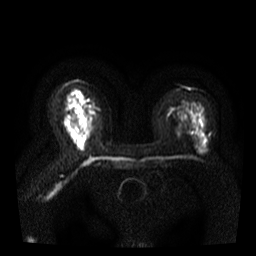
Breast MRI, one axial slice. Slice 20 of 40 in the series (ordered by position). Diffusion-weighted series; image 2 of 4 stored at this slice position (different b-values; order by instance number). 3 T. 5 mm slice thickness. 256 × 256 image matrix. Female patient.
Structures marked on this image (expert manual segmentation):
- tumour on diffusion-weighted imaging: bounding box <74,113,85,128> (left, top, right, bottom; pixels)